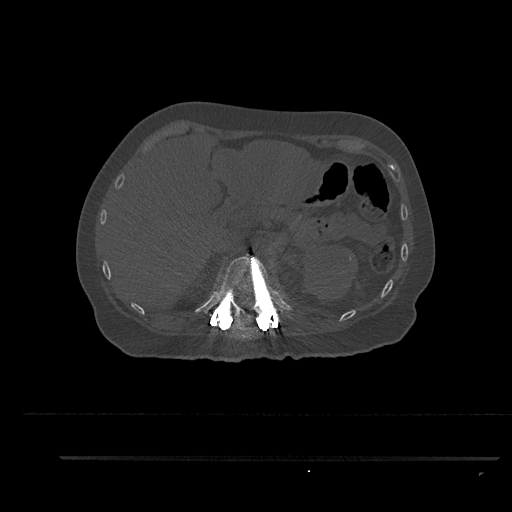
CT including the spine, one axial slice; position 269 of 797 along the scan axis; 120 kVp; bone window (W 1800 / L 400 HU); 512 × 512 image matrix, field of view 408 × 408 mm. Female patient, age 44 years. From the clinical record (not read from this slice): primary cancer: renal; vertebrae with lytic lesions (as recorded): L1.
Outlined on this slice (semi-automatically segmented with operator editing):
- T12 vertebra: bounding box (x1, y1, x2, y2) in pixels: (217, 254, 283, 319)